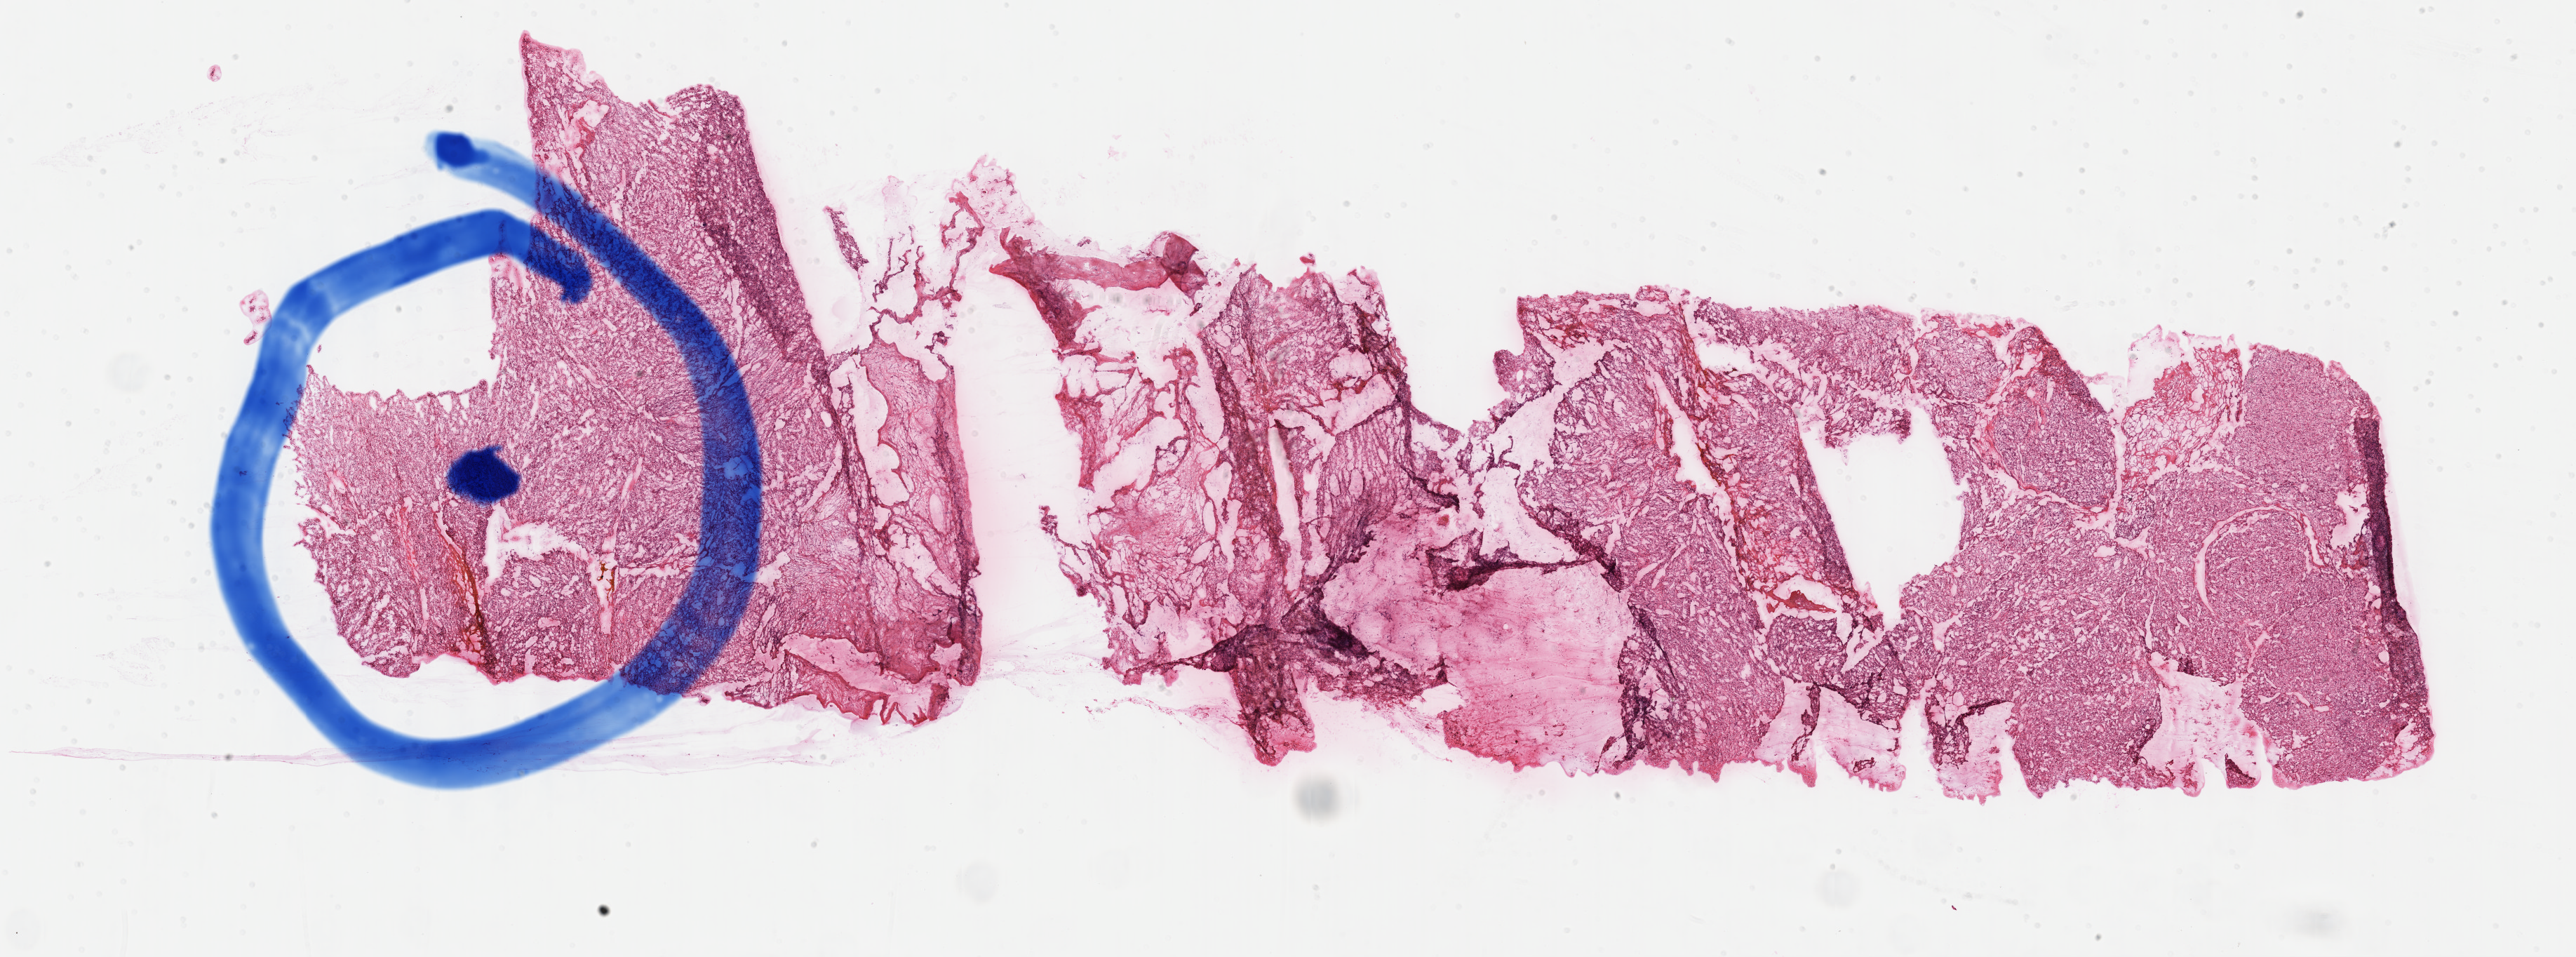
Digitized H&E tissue section (whole slide) — low-resolution overview of the scanned area, about 29.7 x 11.0 mm (slide scanned at 40x). FFPE section. Primary tumour sample from the kidney. Male, age 61 years at initial diagnosis. Histologic grade: G2 (moderately differentiated).
• AJCC pathologic stage: III
• pathologic diagnosis: Clear cell adenocarcinoma, NOS